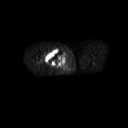
FDG PET of an extremity soft-tissue mass (from a PET/CT study), one axial slice. Position 249 of 311 along the scan axis. 3.27 mm slice thickness. 128 × 128 image matrix. Male patient, age 50 years. From the clinical record (not read from this slice): histological type: undifferentiated - pleiomorphic; grade: high; site of the primary tumour: right thigh.
Structures marked on this image (expert contour drawn on MRI and transferred to this co-registered scan by the dataset authors):
- gross tumour volume including surrounding oedema: bounding box [x1, y1, x2, y2] px = [41, 49, 63, 66]
- gross tumour volume (mass): [45, 49, 63, 66]